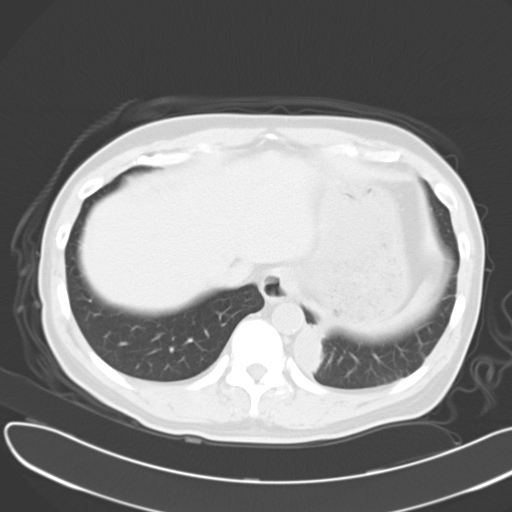
Chest CT, one axial slice; position 7 of 30 along the scan axis; 120 kVp; lung window (W 1500 / L -600 HU); 10 mm slice thickness; 512 × 512 image matrix, field of view 376 × 376 mm. Patient: male, 55 years. Case-level facts recorded for this patient, not image findings: clinical TNM (as recorded): T2 N3 M0; histopathological grade: G3.
Outlined on this slice (rectangle marked by the reading radiologist):
- lung tumour (recorded histology: small cell carcinoma): box from (x=287, y=319) to (x=322, y=374) px